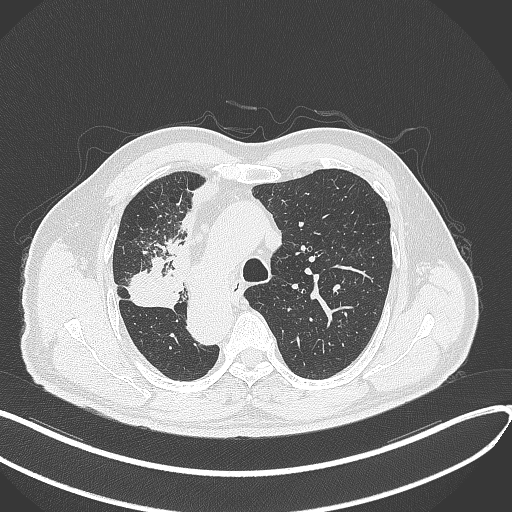
Chest CT, one axial slice; slice 226 of 300 in the series (ordered by position); reconstruction kernel B70f; lung window (W 1500 / L -600 HU); 1 mm slice thickness; 512 × 512 image matrix, field of view 400 × 400 mm. Male patient, age 67 years. From the clinical record (not read from this slice): clinical TNM (as recorded): T2a N0 M0.
Annotated regions visible in this slice (bounding box drawn by a radiologist):
- lung tumour (recorded histology: squamous cell carcinoma): box from (x=126, y=253) to (x=186, y=312) px